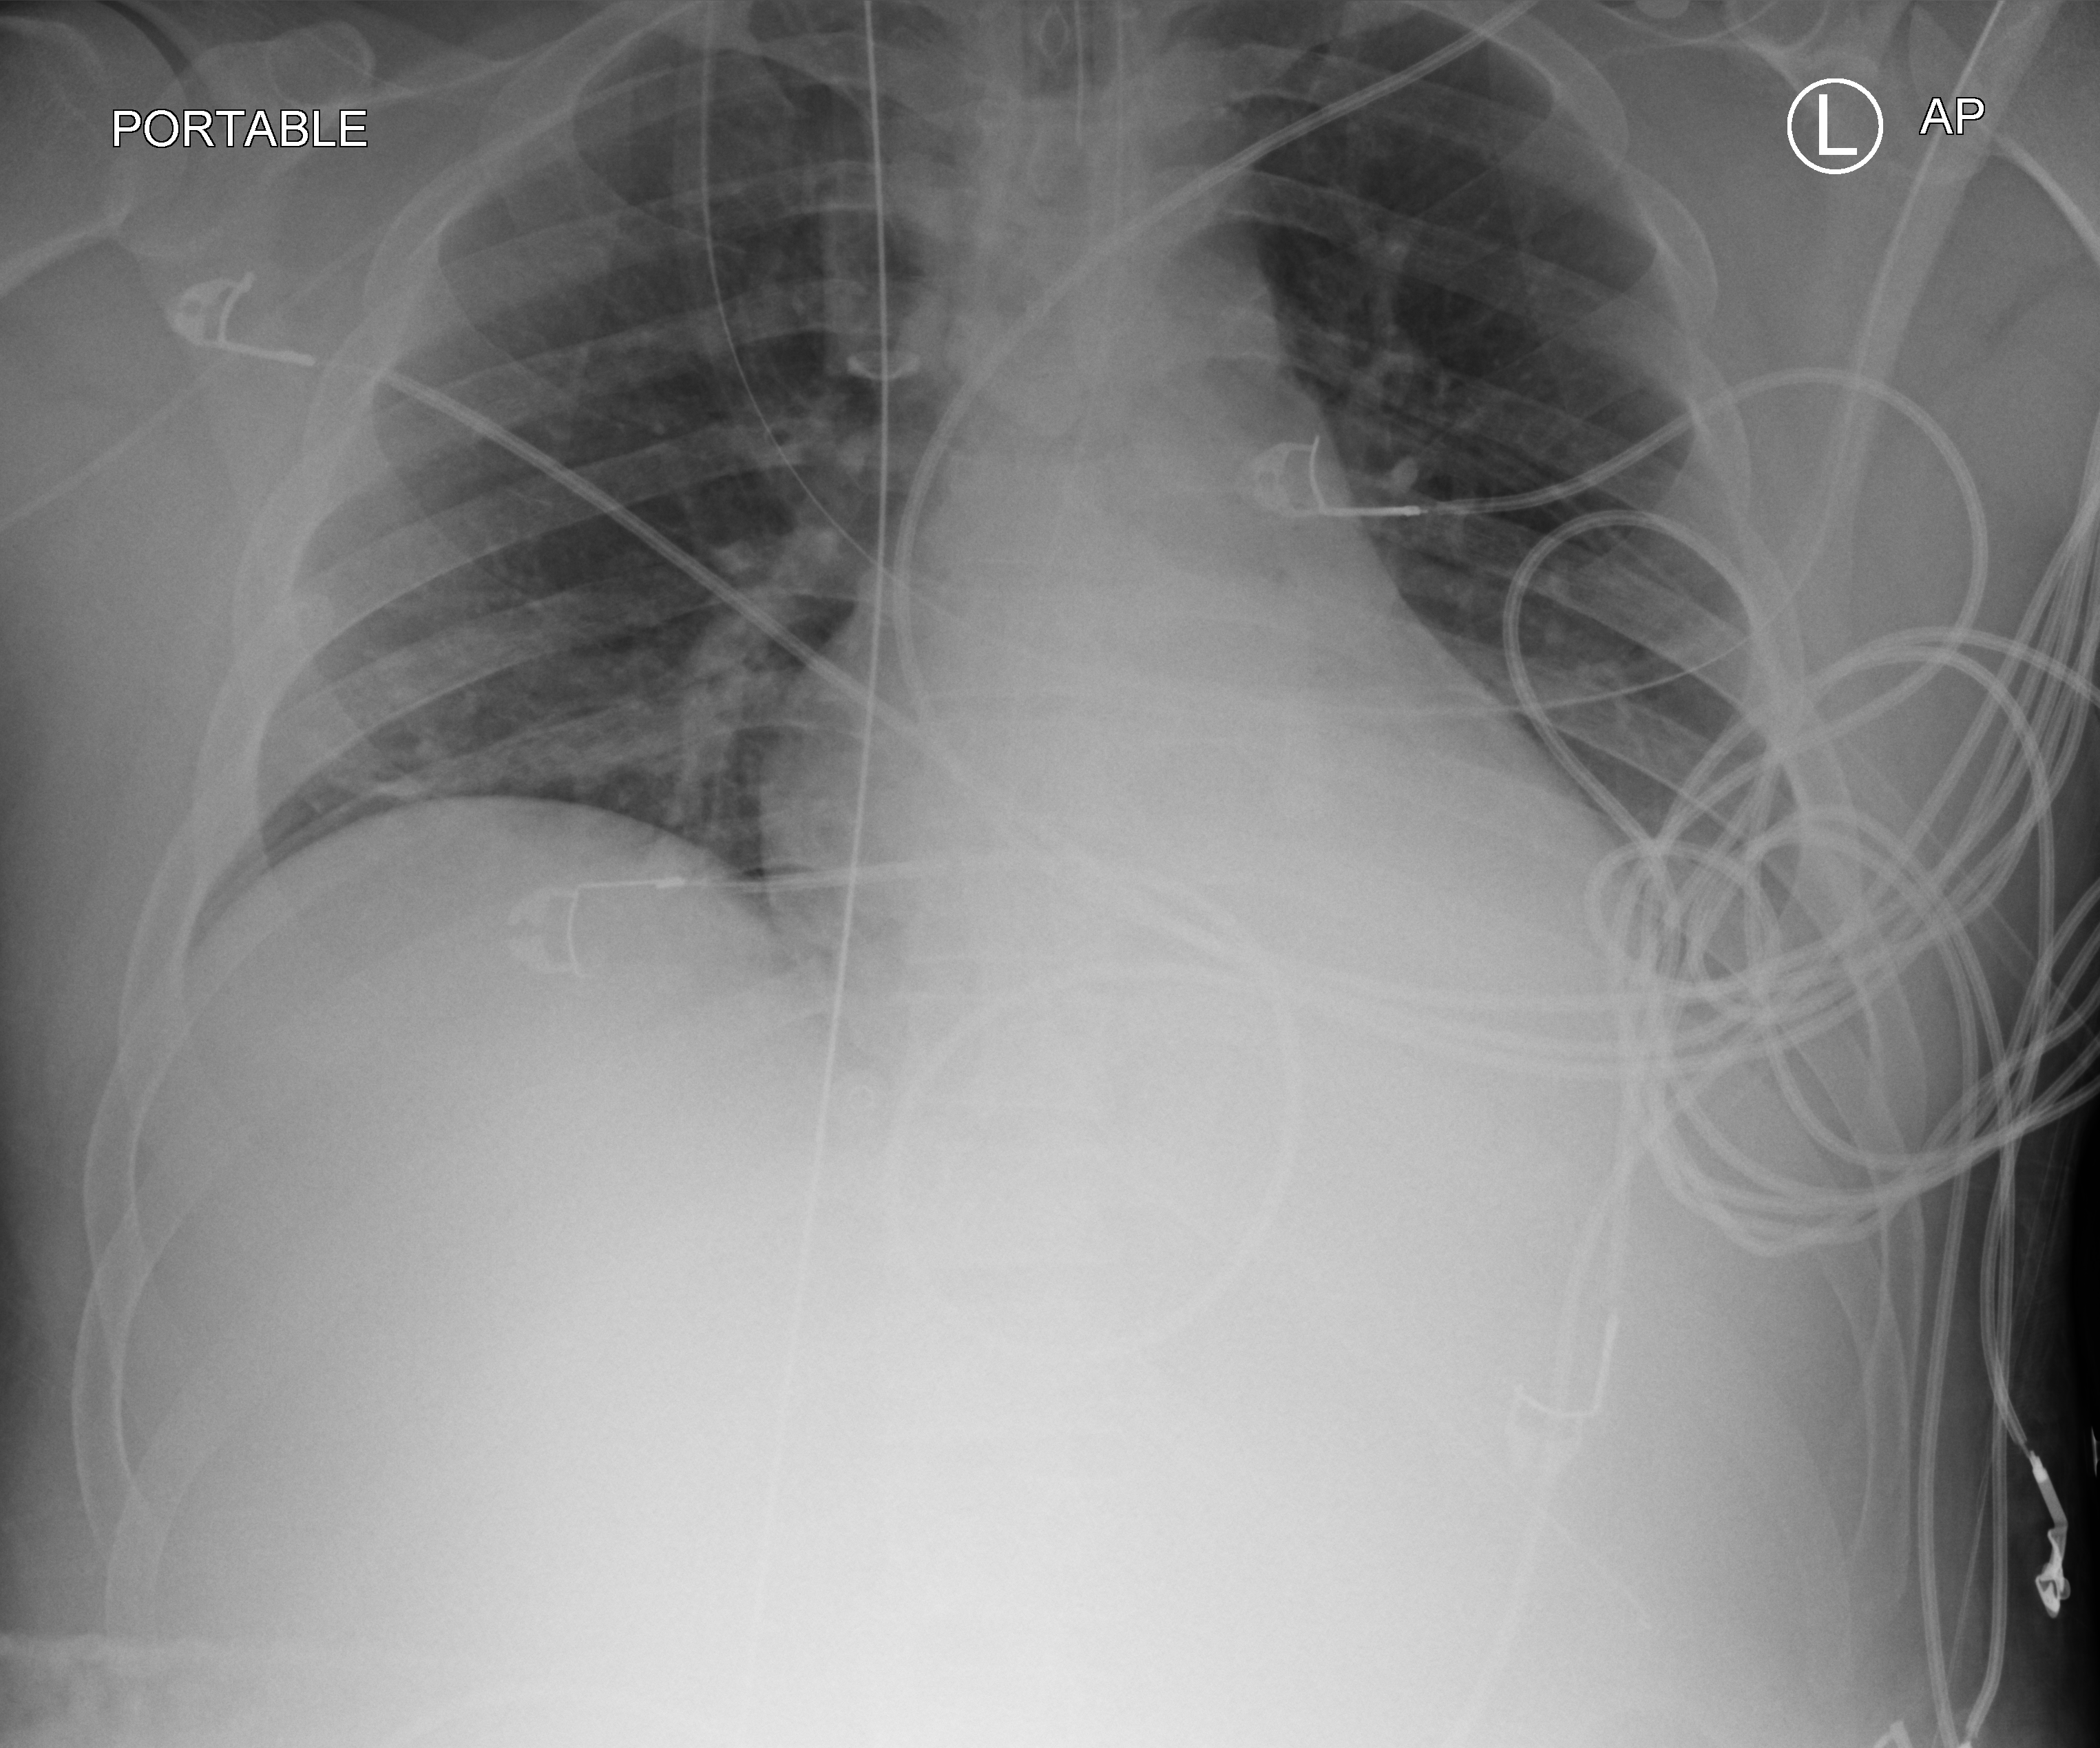
Portable chest radiograph; anteroposterior (AP) projection. Male patient hospitalised with COVID-19, age 18–59 years.
Admission-level facts for this patient (not findings on this image; timing relative to this image not recorded):
- admitted to intensive care during this hospital stay: yes
- hypertension (admission record): yes
- COPD (admission record): no